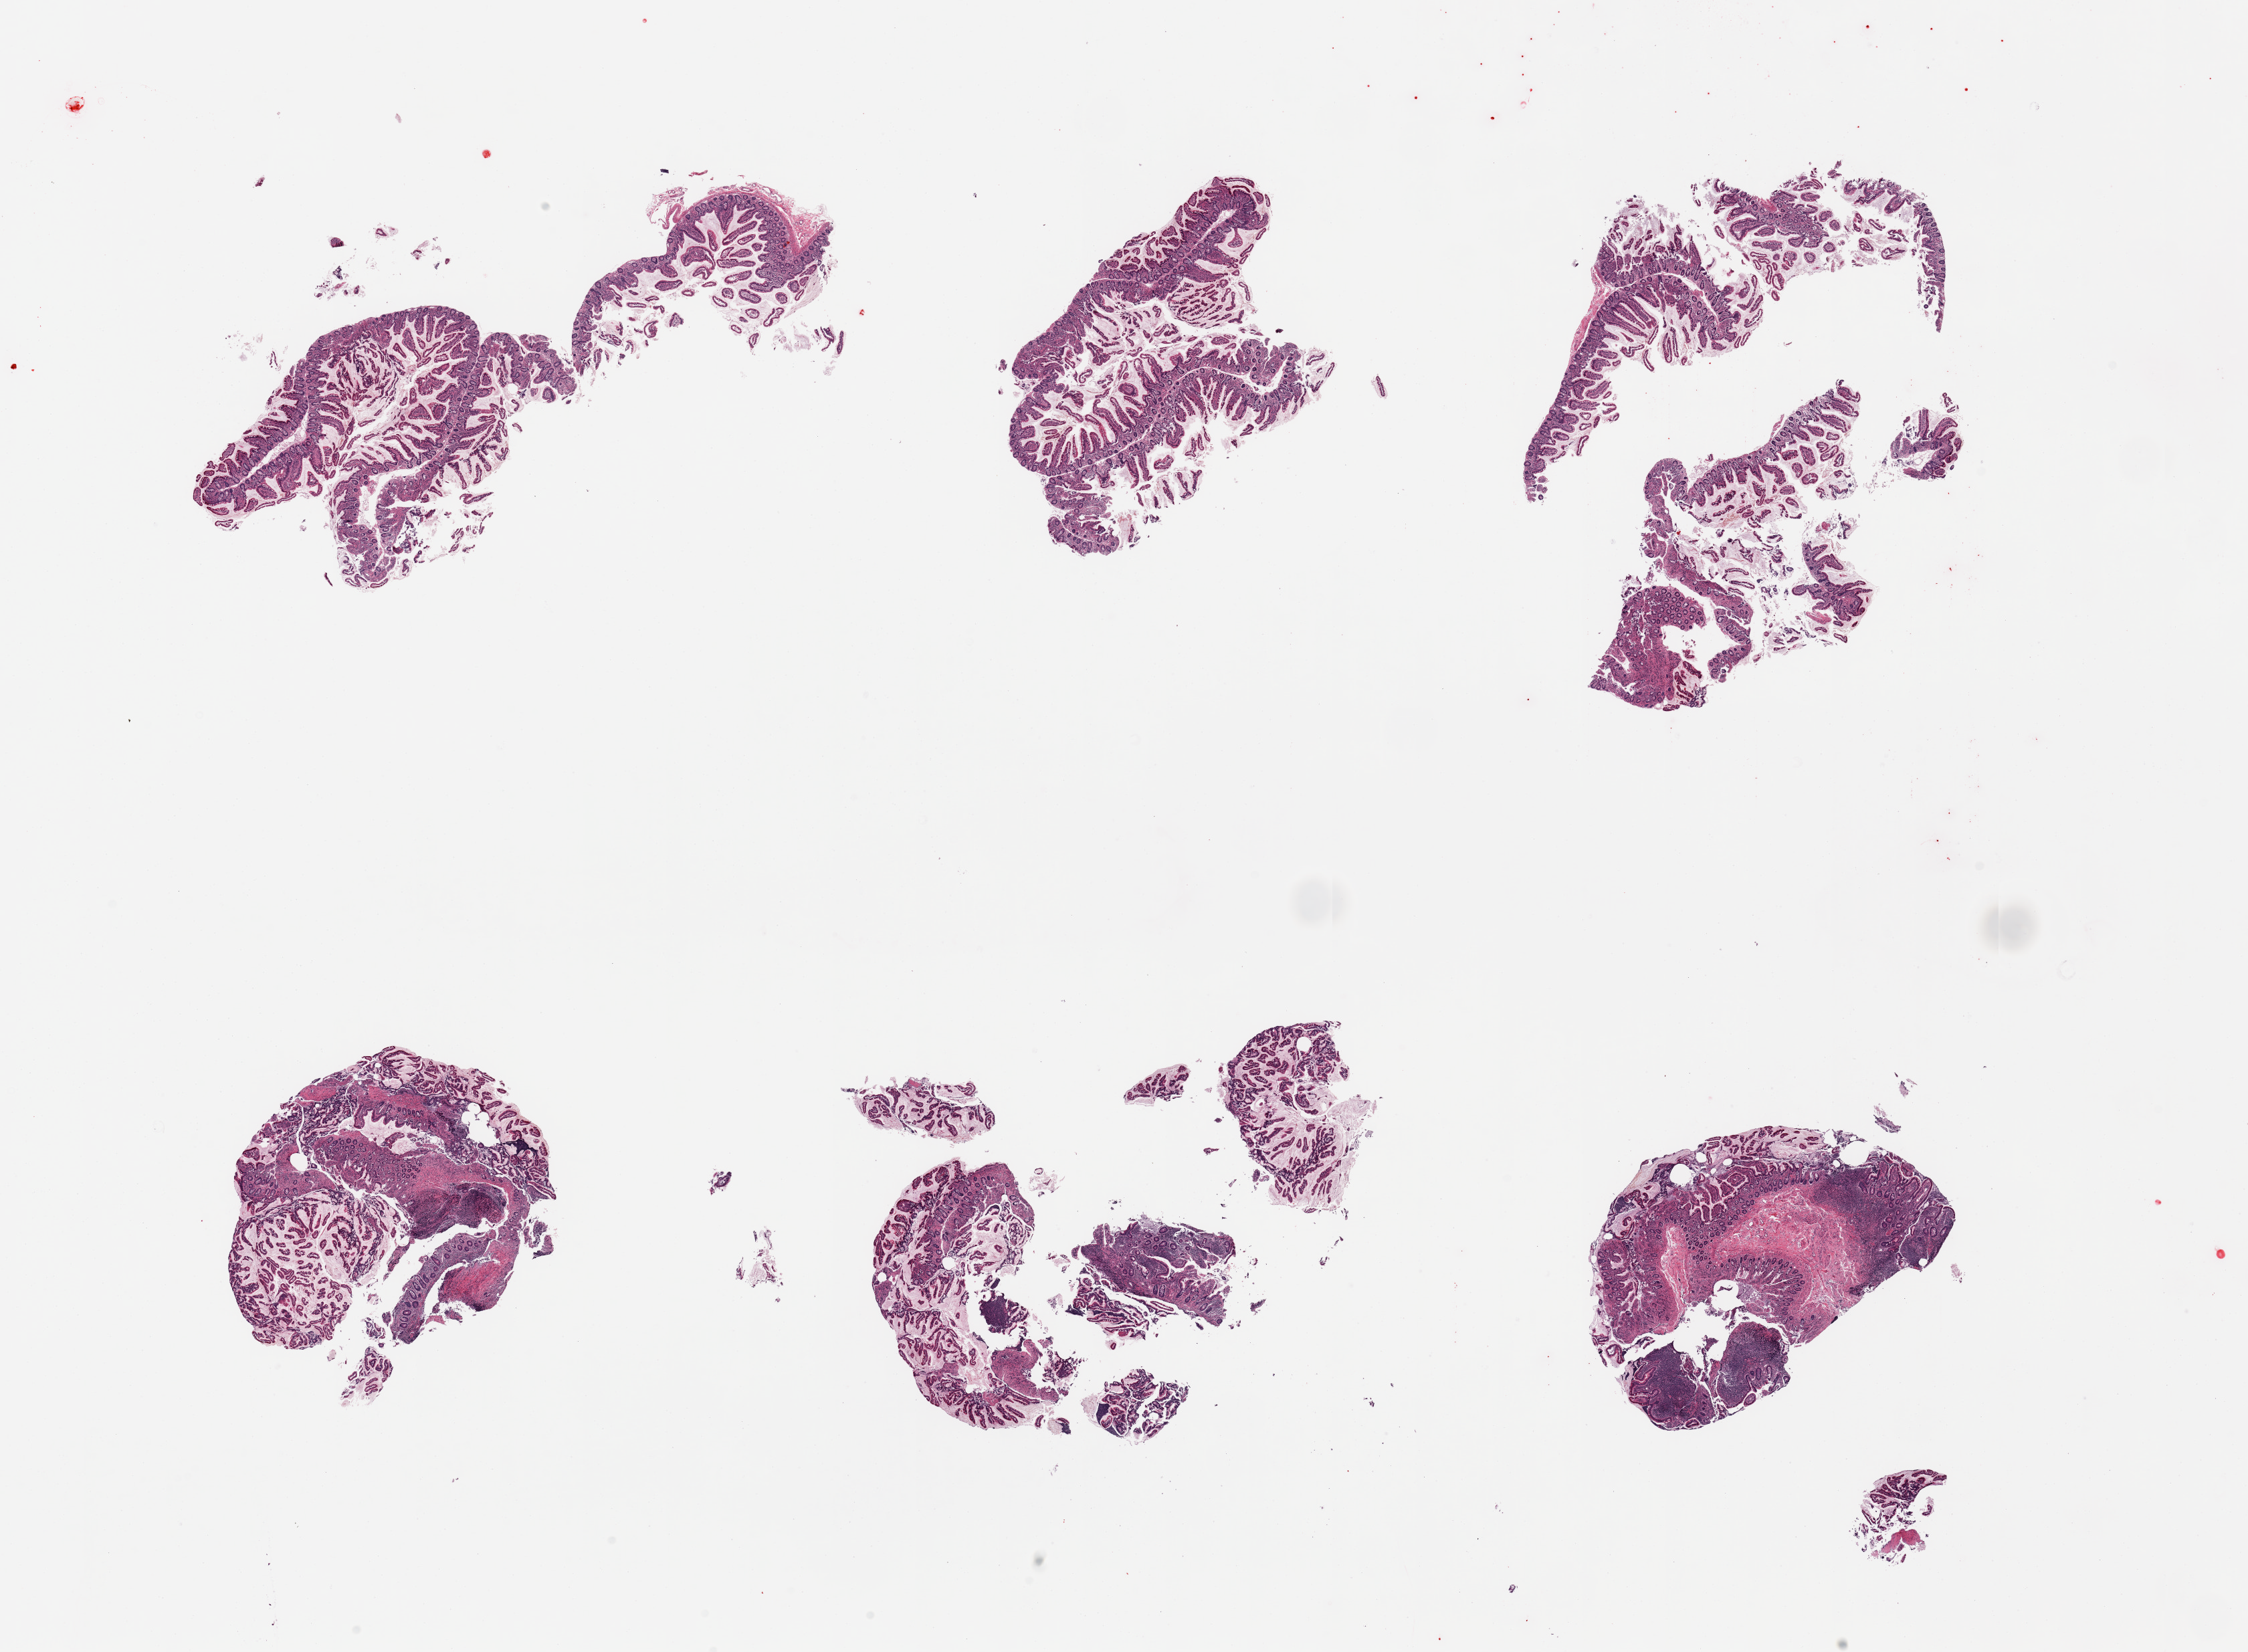
Whole-slide image, haematoxylin and eosin stain, brightfield — low-resolution overview of the scanned area, about 26.6 x 19.5 mm; PAXgene-fixed, paraffin-embedded tissue; section of ileum (target tissue); donor tissue sample. Donor: male.
Review note (as recorded): 6 pieces; well preserved mucosa with several lymphoid nodules.